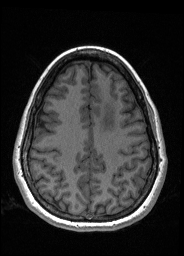
Pre-operative brain MRI before brain-tumour surgery, one axial slice. Slice 62 of 176 in the series (ordered by position). T1-weighted post-contrast. 1 mm slice thickness. 184 × 256 image matrix. Case-level facts recorded for this patient, not image findings: histopathology: Oligodendroglioma; WHO grade: 2; IDH mutation: yes; tumour location: Left Frontal.
Structures marked on this image (expert manual segmentation):
- tumour: bounding box <100,98,116,131> (left, top, right, bottom; pixels)